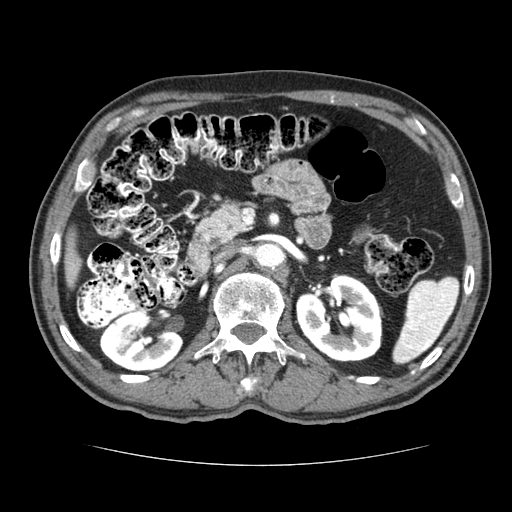
Contrast-enhanced abdominal CT (liver protocol), one axial slice. Slice 28 of 79 in the series (ordered by position). Reconstruction kernel STANDARD. 120 kVp. Soft-tissue window (W 400 / L 40 HU). 2.5 mm slice thickness. 512 × 512 image matrix. From the clinical record (not read from this slice): diagnosis: hepatocellular carcinoma (patient treated with transarterial chemoembolisation; whether this scan precedes or follows treatment is not stated here); TNM stage (as recorded): Stage-I; Child-Pugh class: A.
Annotated regions visible in this slice (semi-automatically segmented with operator editing):
- liver parenchyma outside the tumour (the mass and vessels are separate outlines, so this box may not span the whole liver): bounding box <64,229,80,287> (left, top, right, bottom; pixels)